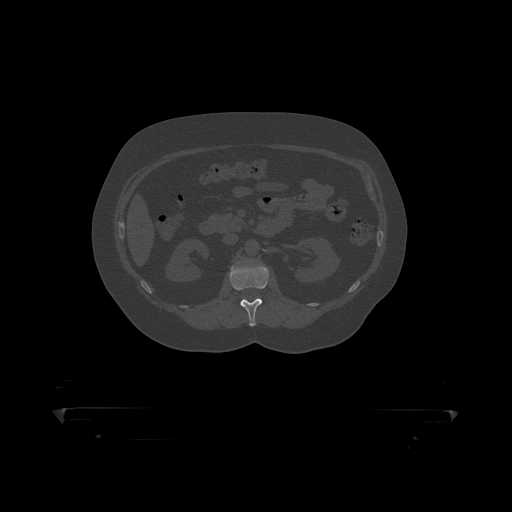
CT including the spine, one axial slice; slice 137 of 390 in the series (ordered by position); reconstruction kernel STANDARD; 120 kVp; bone window (W 1800 / L 400 HU); 1.25 mm slice thickness; 512 × 512 image matrix, field of view 650 × 650 mm. Male patient, age 60 years. Case-level facts recorded for this patient, not image findings: primary cancer: prostate.
Structures marked on this image (semi-automatic segmentation, software-assisted and operator-edited):
- L1 vertebra: bounding box <230,261,269,319> (left, top, right, bottom; pixels)